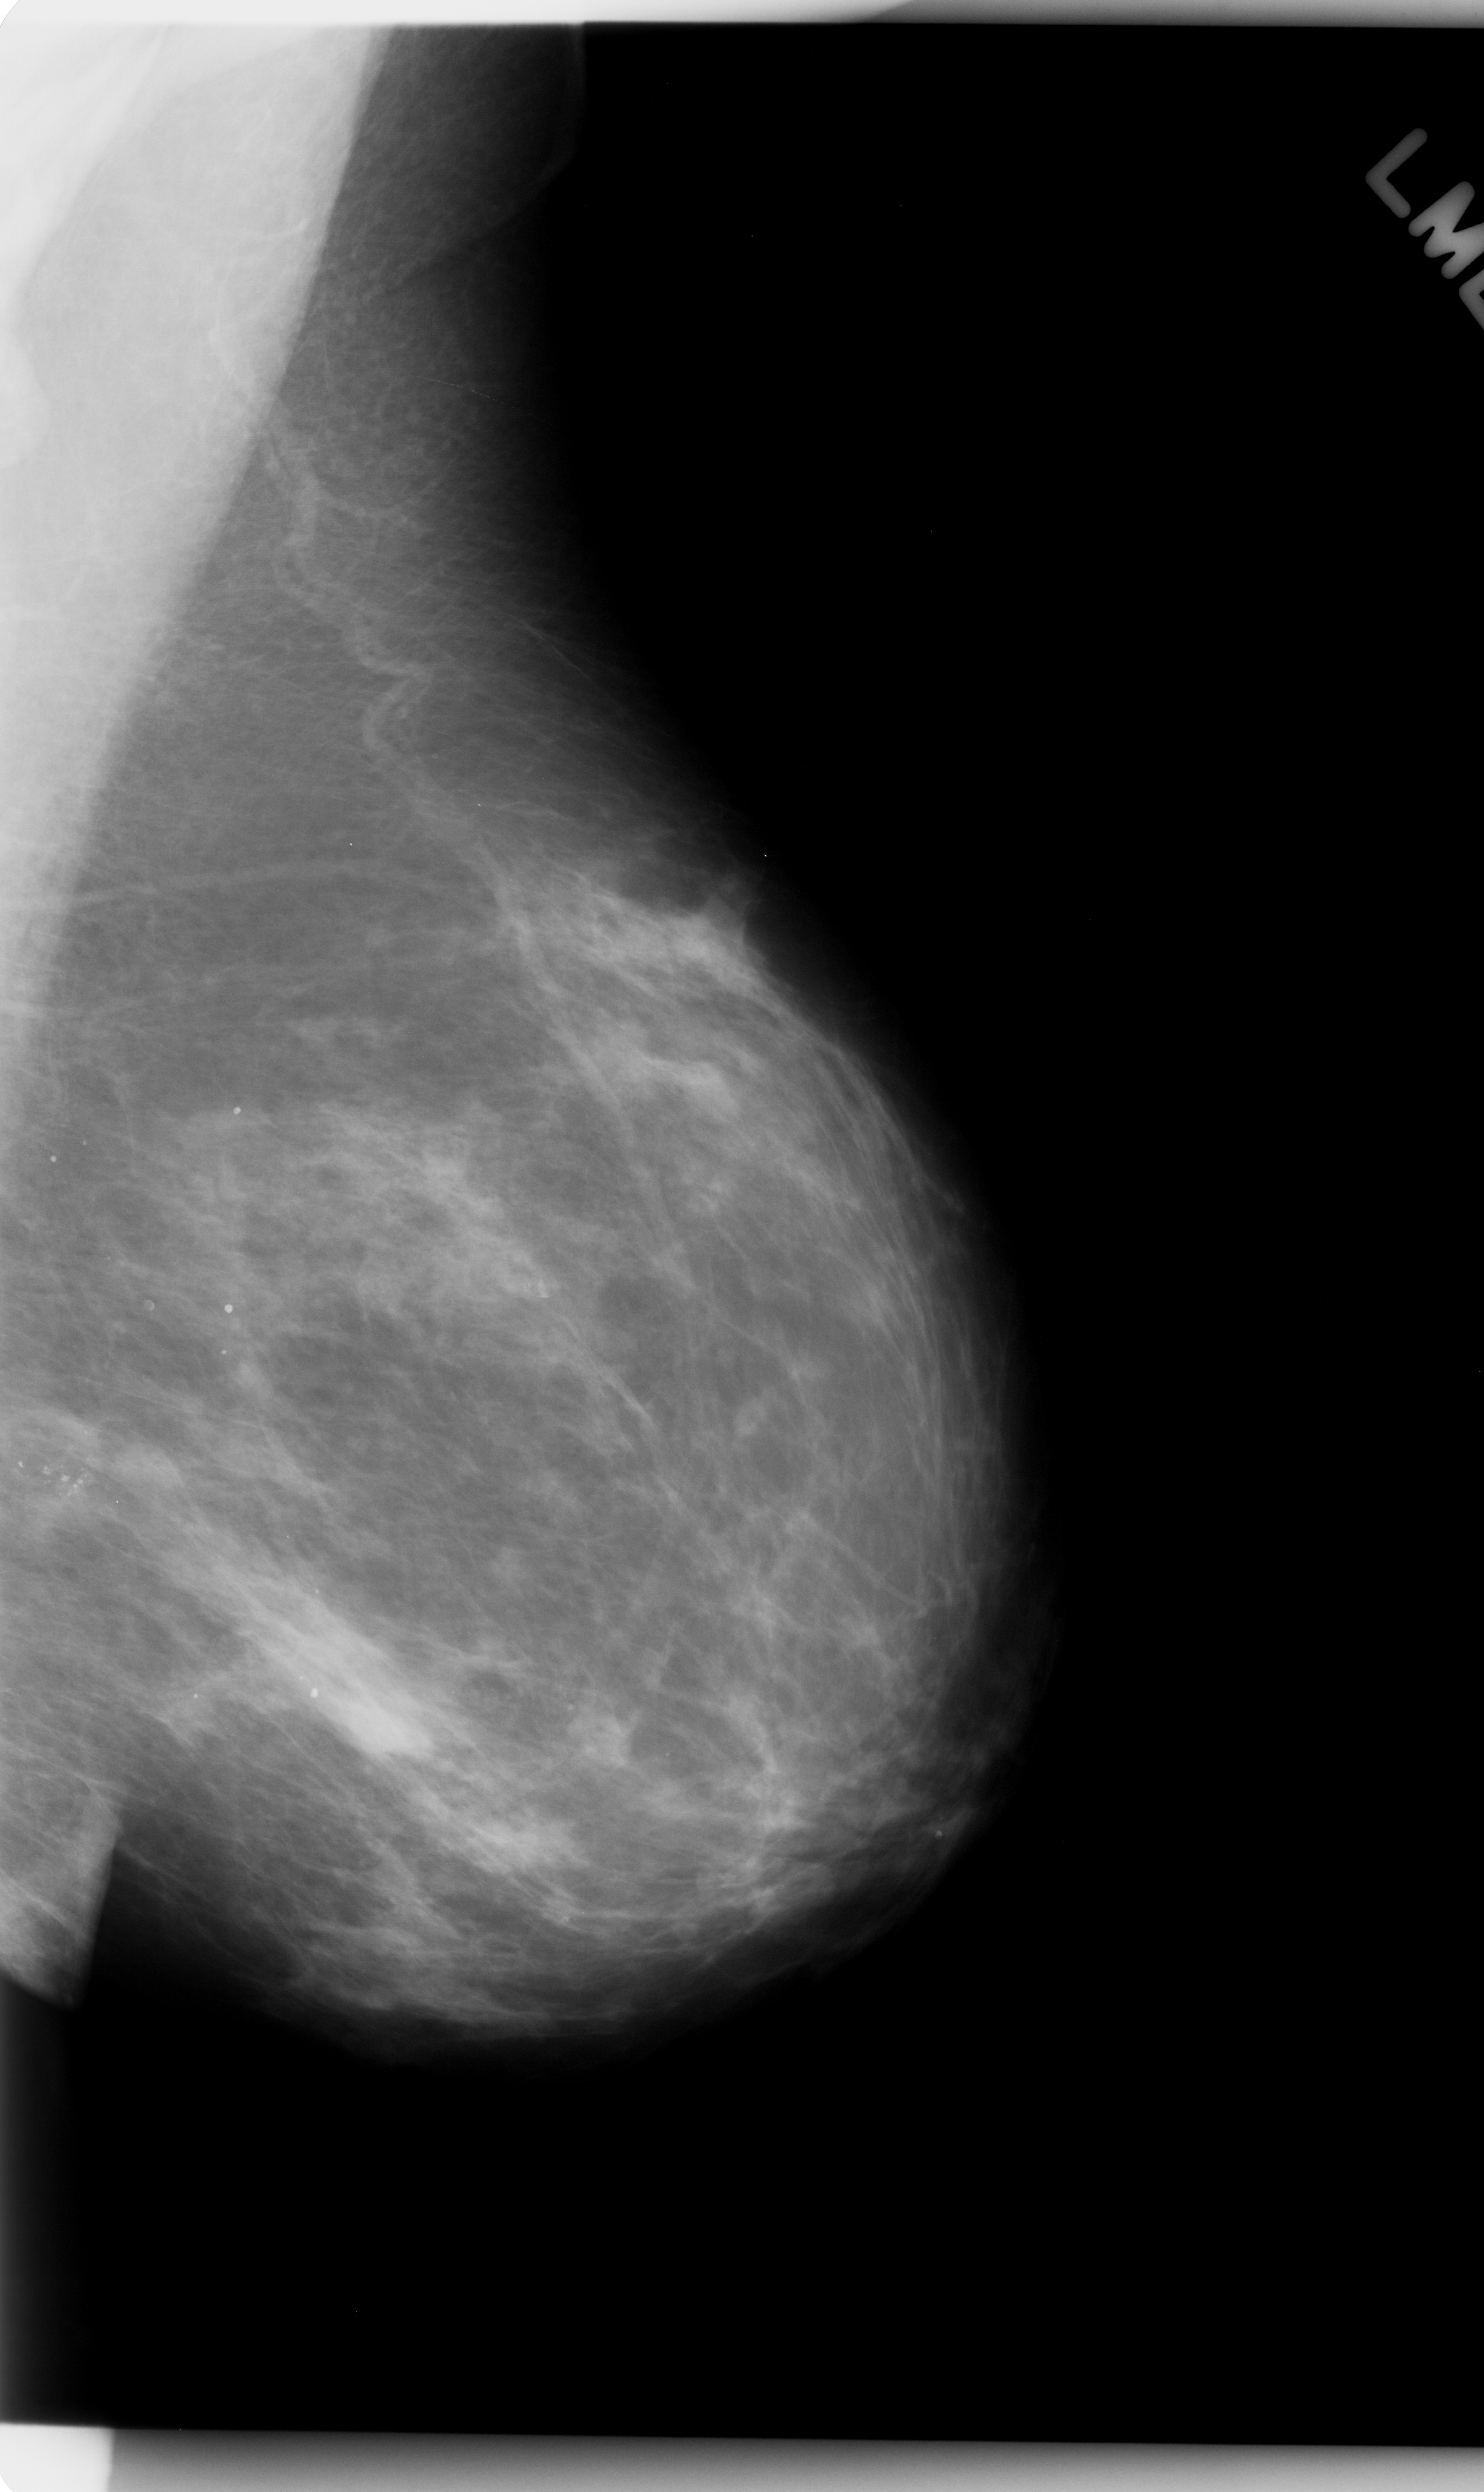
Digitized screen-film mammogram; left breast; mediolateral oblique (MLO) view; BI-RADS breast density category 2 (scale 1–4).
- Marked findings (only marked abnormalities are described; nothing is implied about the rest of the image): calcifications, morphology amorphous, distribution clustered; BI-RADS assessment category 4; pathology (as recorded): benign.